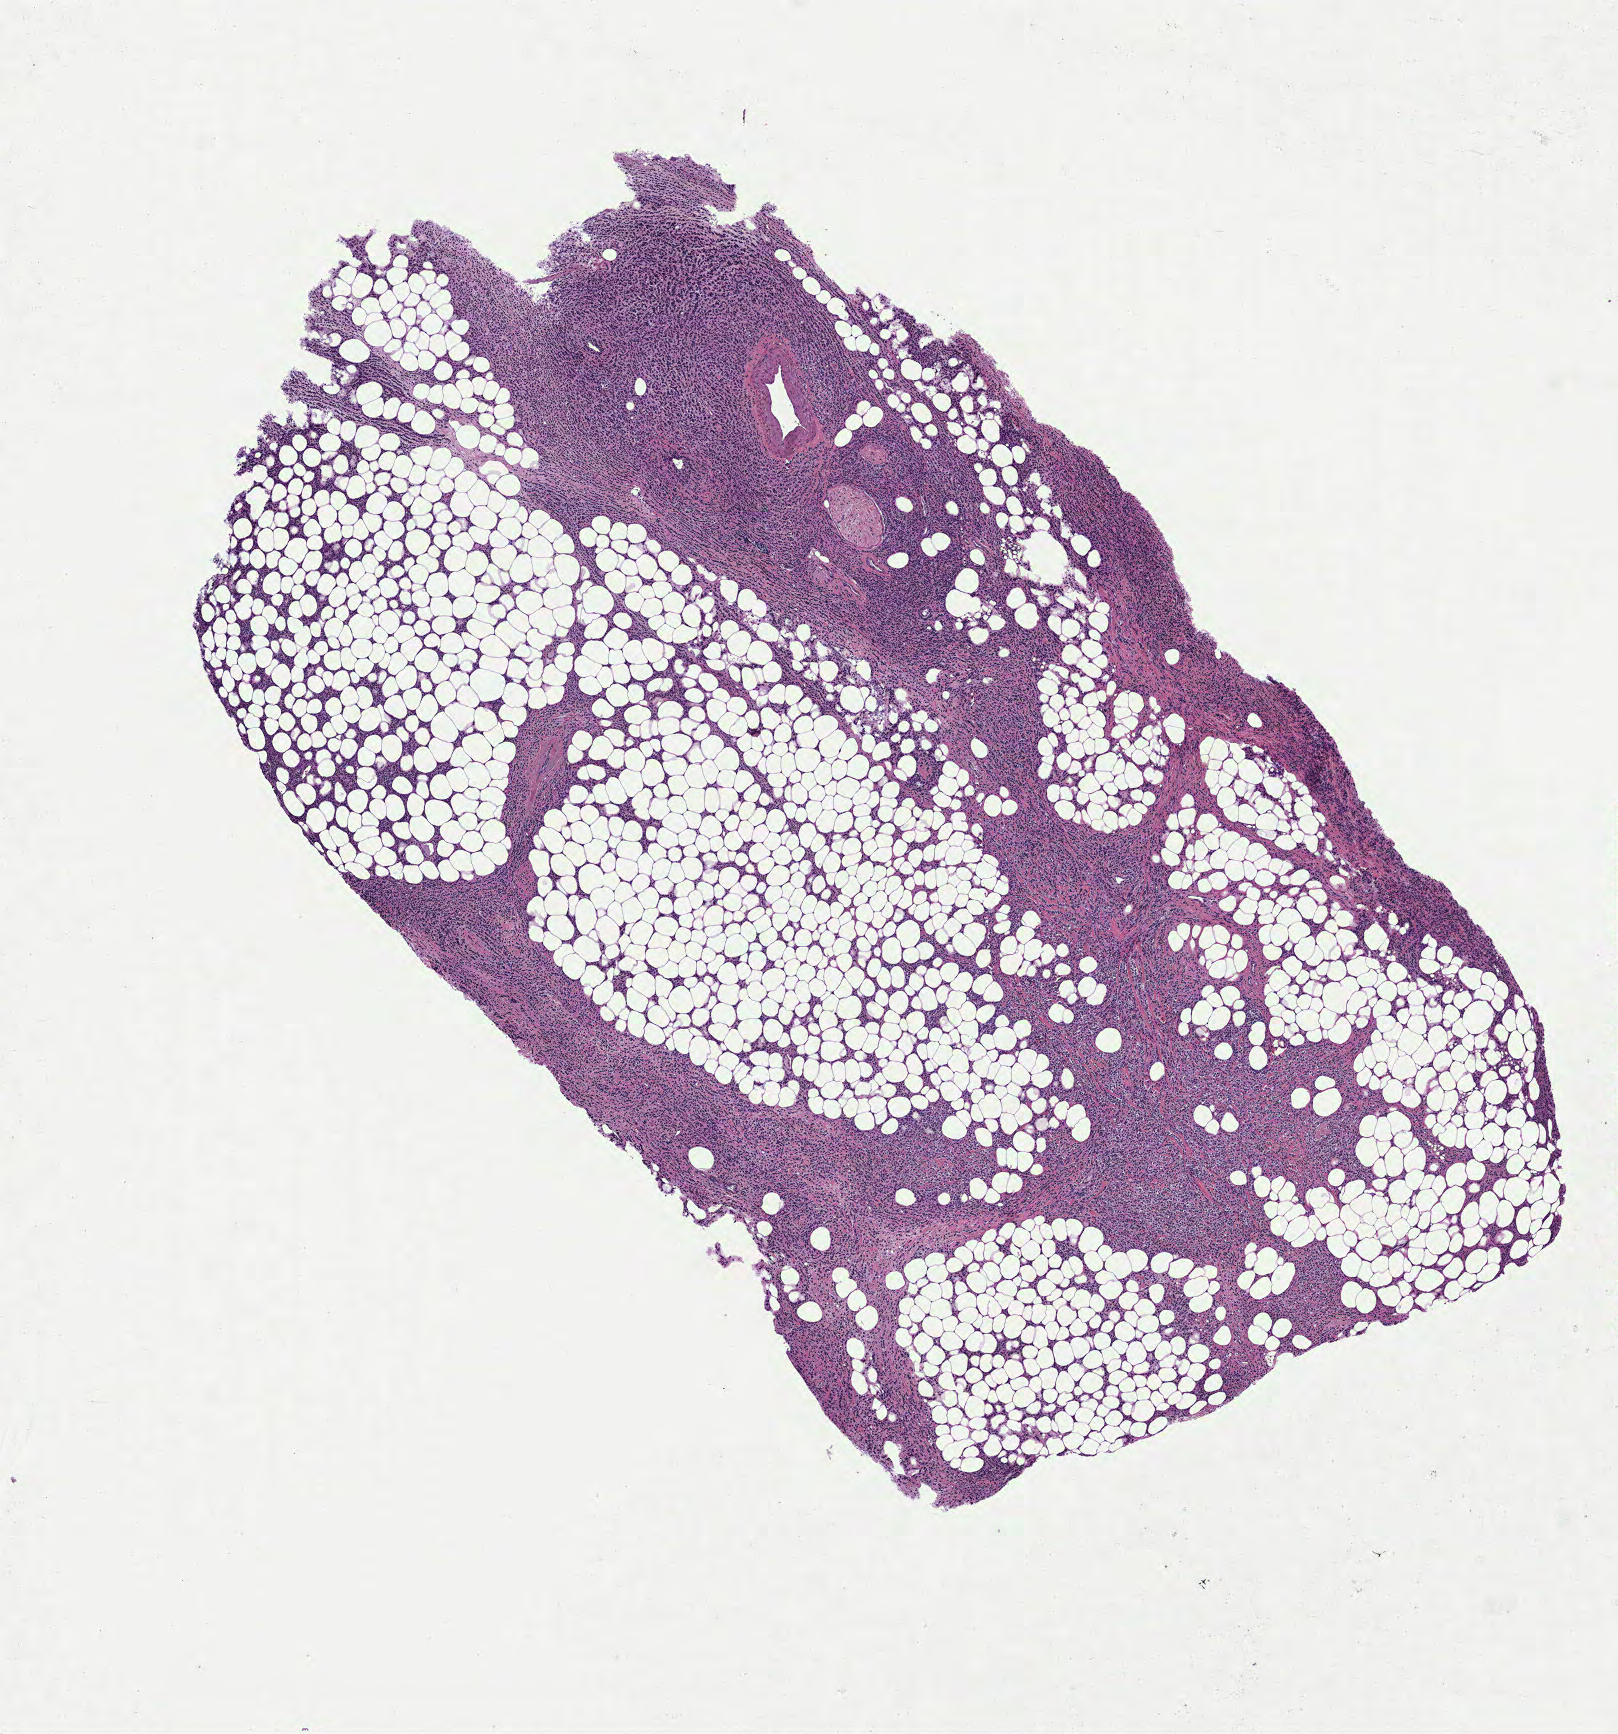
Whole-slide histology image, H&E-stained, a low-resolution overview of the entire scanned area, about 6.5 x 7.0 mm; formalin-fixed paraffin-embedded (FFPE) diagnostic section; breast, primary tumour sample. Patient: female, age at initial diagnosis 63 years.
* laterality: right
* lymph nodes positive (case pathology): 0 of 1 examined
* TNM: T3 N0 M0
* AJCC pathologic stage: IIB (7th edition)
* histologic diagnosis: Lobular carcinoma, NOS